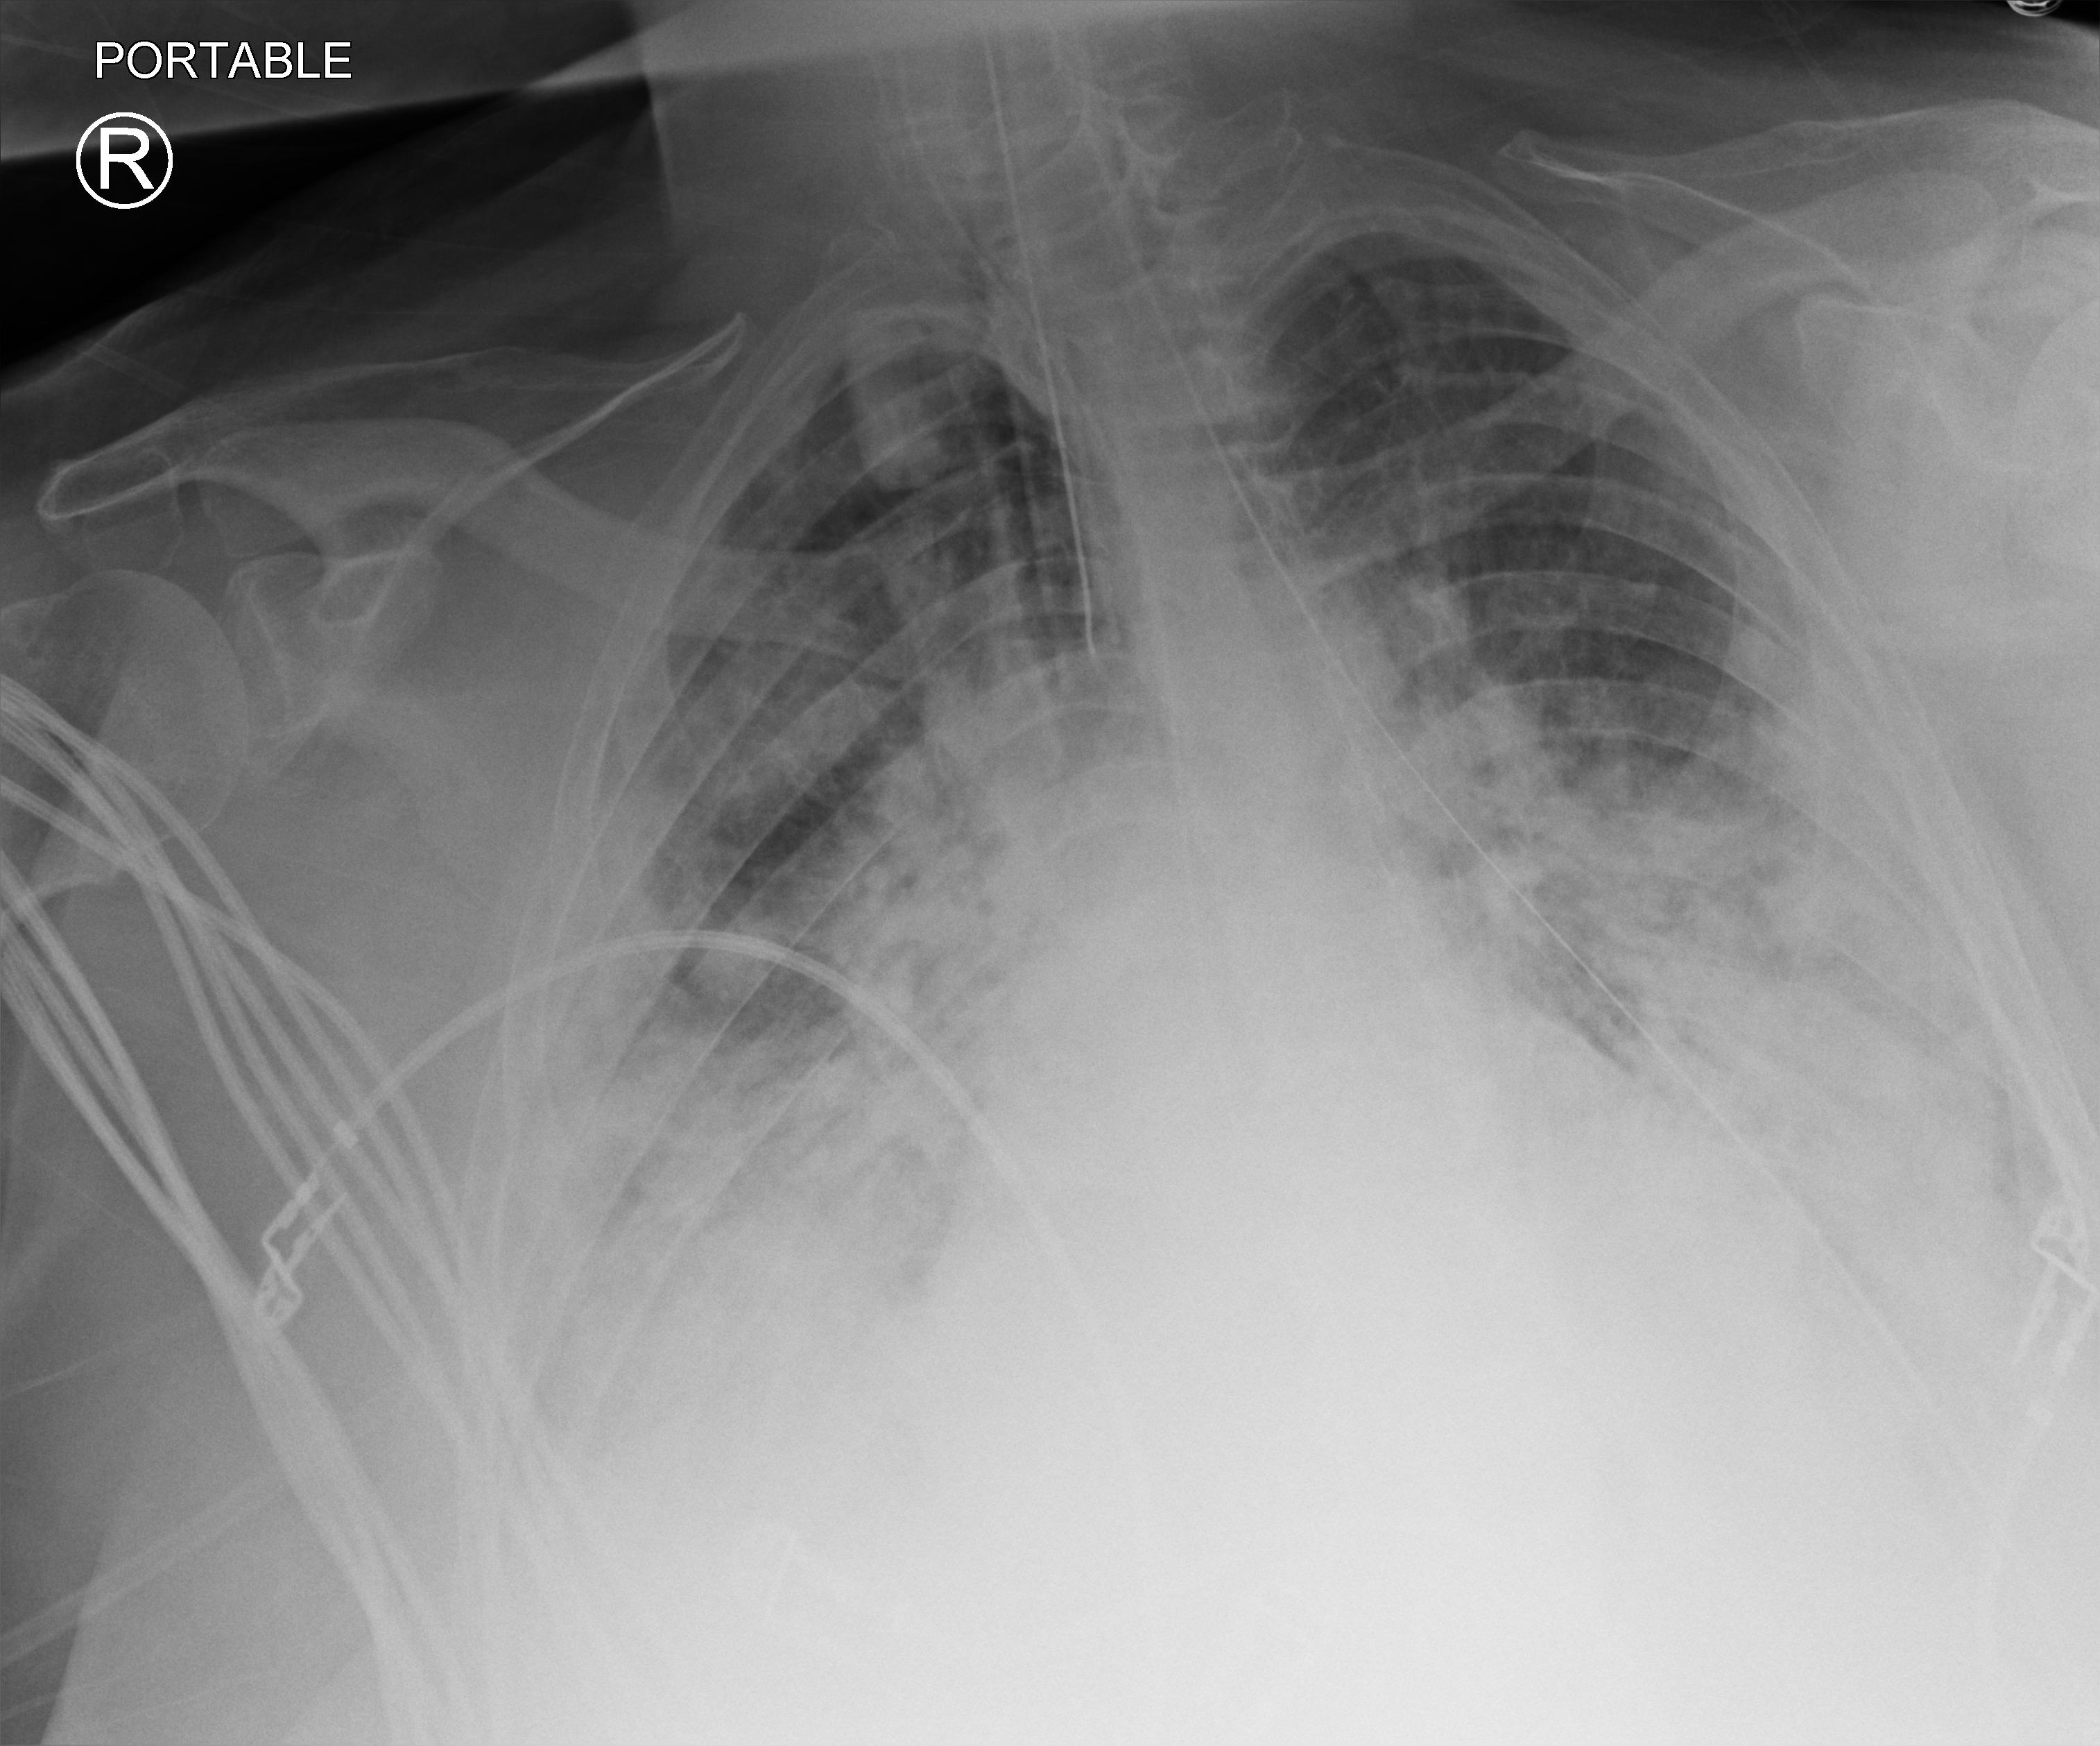
Bedside chest radiograph (computed radiography); anteroposterior (AP) projection. Male patient hospitalised with COVID-19, age 60–74 years.
Admission-level facts for this patient (not findings on this image; timing relative to this image not recorded):
- mechanically ventilated during this hospital stay: yes